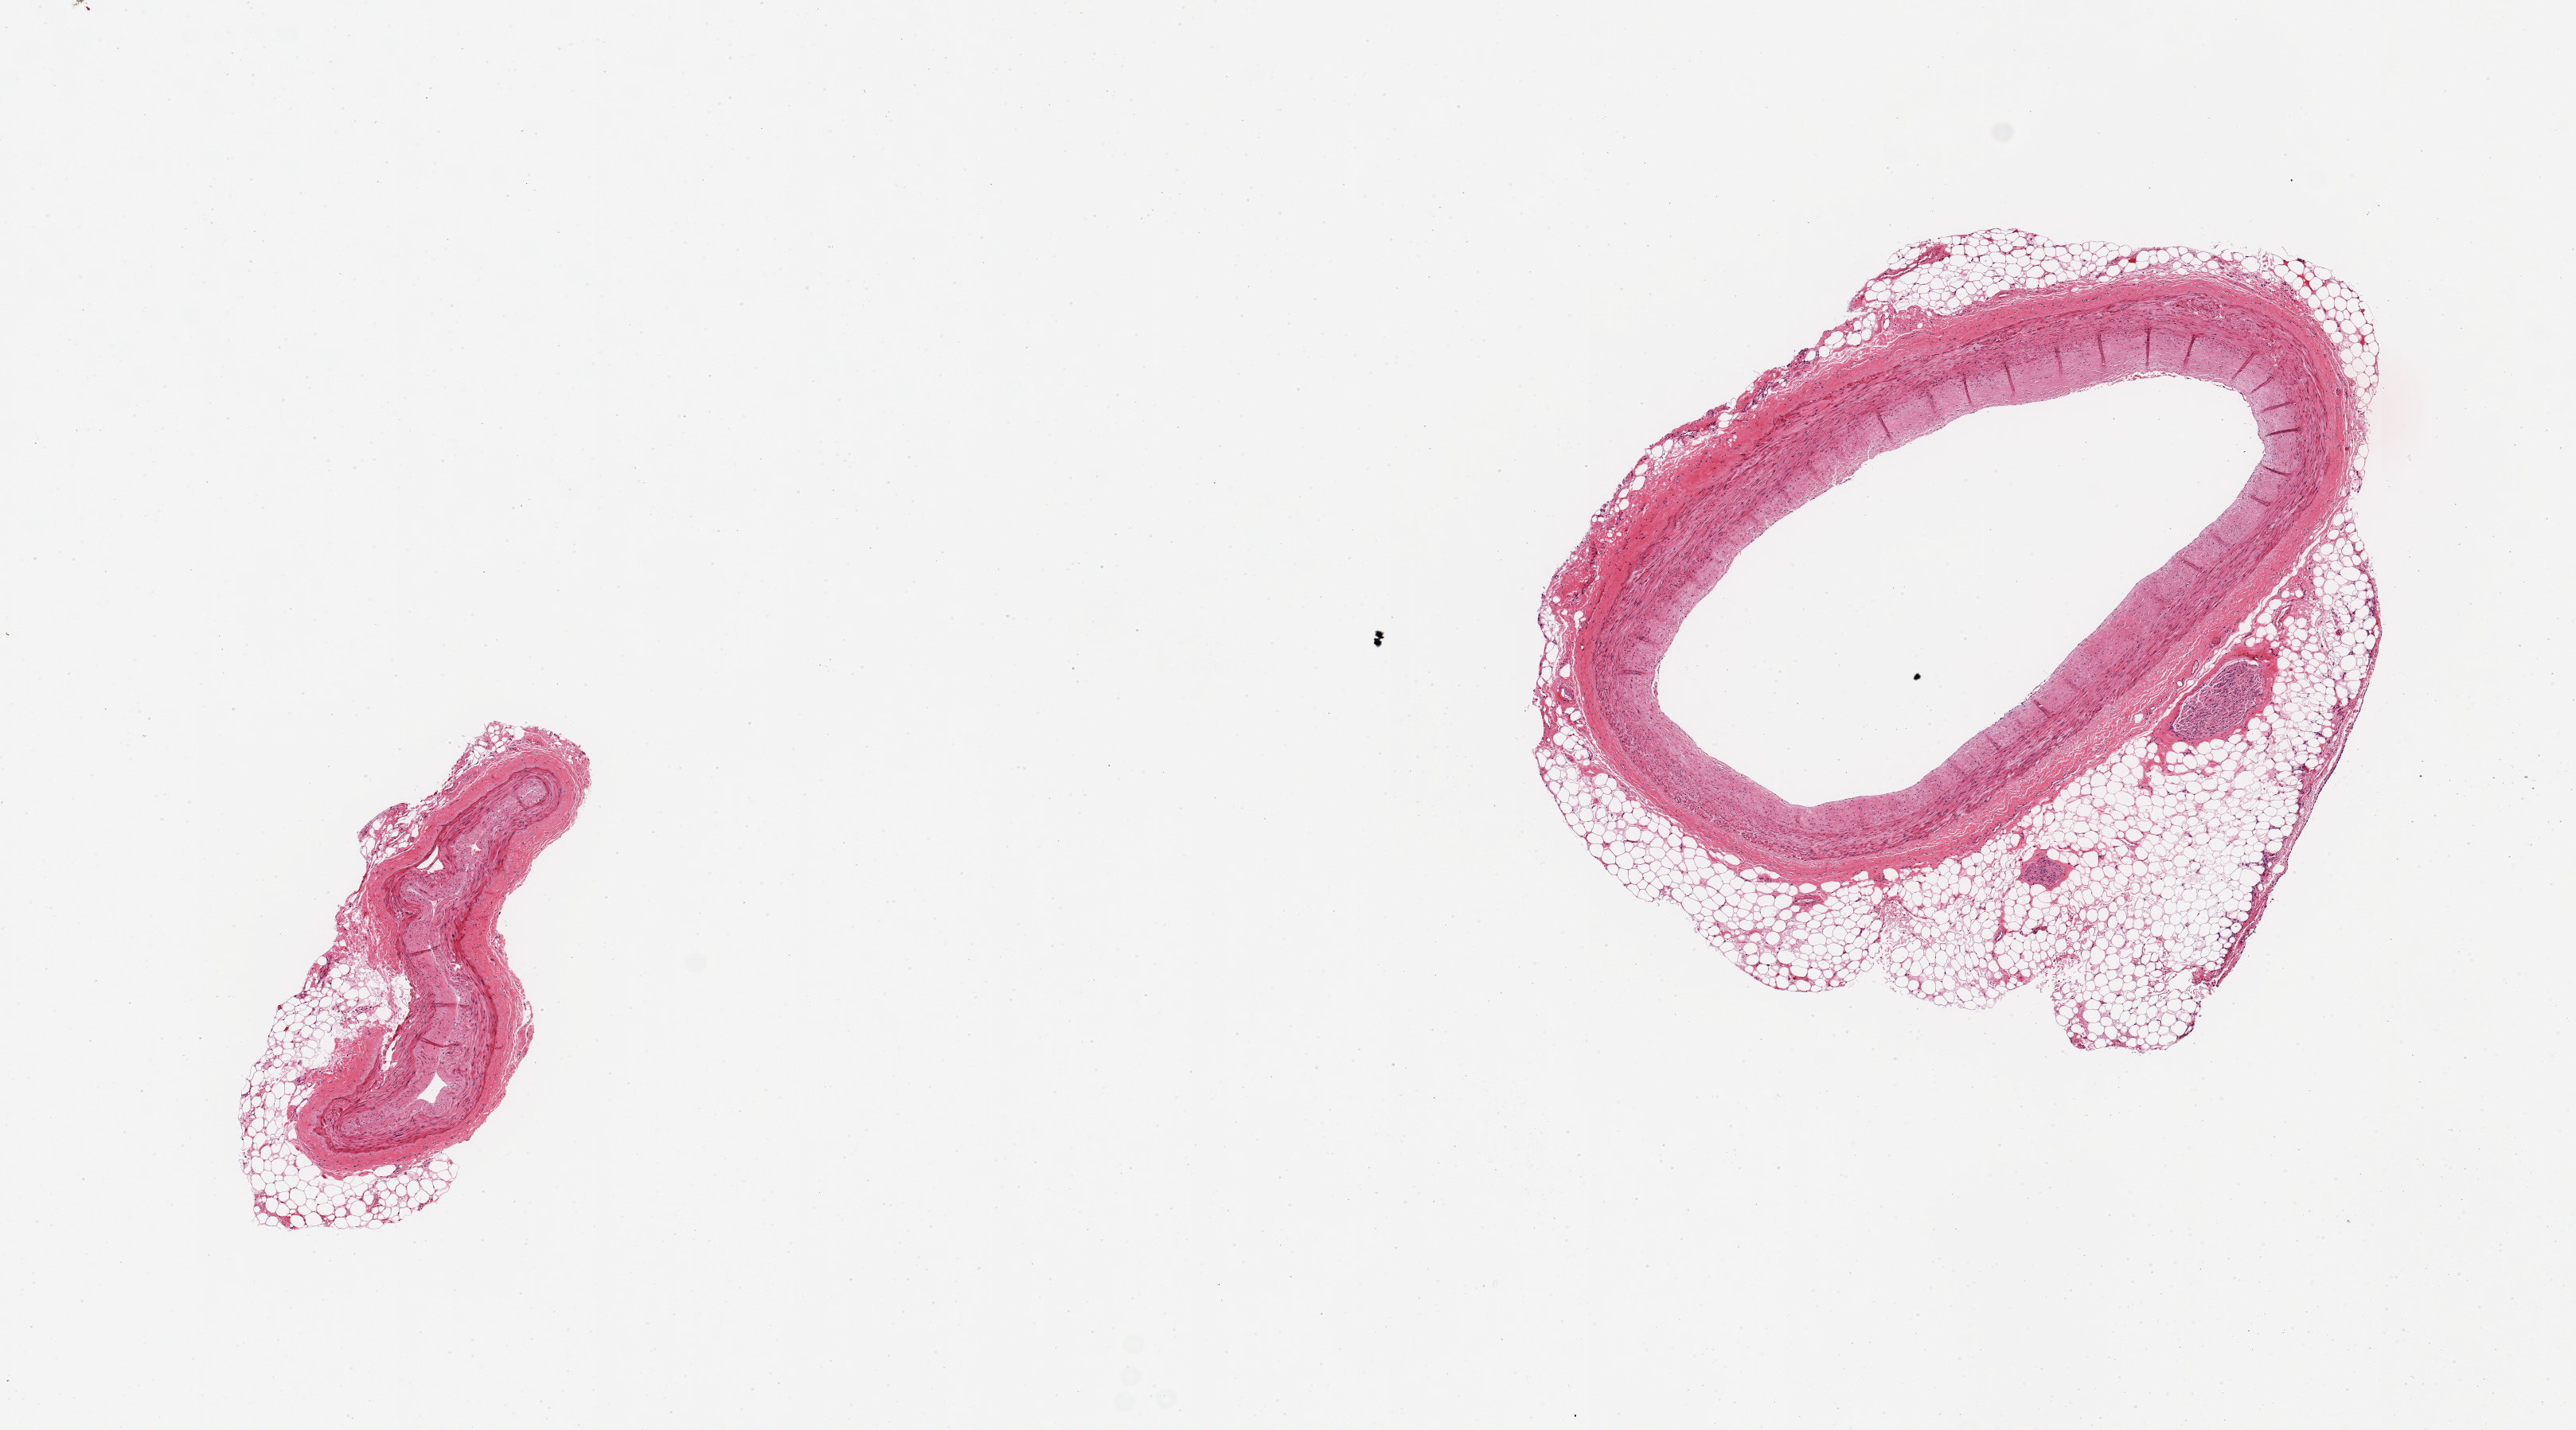
Haematoxylin and eosin whole-slide image, a low-resolution overview of the entire scanned area, about 12.8 x 7.1 mm (from a 20x scan); PAXgene-fixed, paraffin-embedded tissue; target tissue: coronary artery; donor tissue sample. Donor: male.
Reviewer comment on this tissue sample: 2 pieces, discontinuous rim of adherent fat/peripheran nerve, up to ~1.2mm.